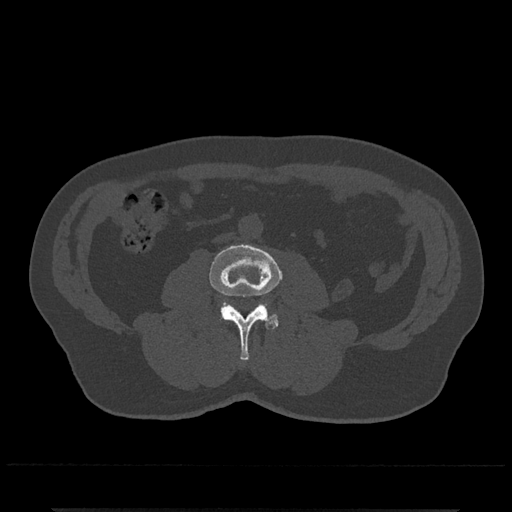
CT including the spine, one axial slice; position 209 of 797 along the scan axis; reconstruction kernel Br40s/3; bone window (W 1800 / L 400 HU); 0.5 mm slice thickness; 512 × 512 image matrix, field of view 393 × 393 mm. Male patient, age 67 years. Case-level facts recorded for this patient, not image findings: primary cancer: prostate.
Structures marked on this image (semi-automatic segmentation, software-assisted and operator-edited):
- L3 vertebra: bounding box (x1, y1, x2, y2) in pixels: (209, 244, 282, 361)
- L4 vertebra: (222, 302, 279, 326)